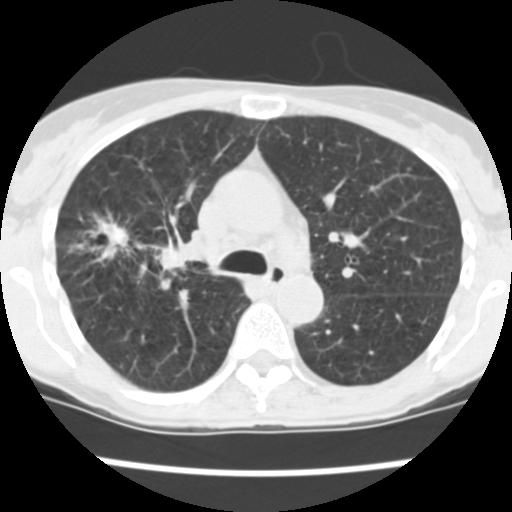
Low-dose screening chest CT, one axial slice; position 163 of 252 along the scan axis; reconstruction kernel STANDARD; 120 kVp; lung window (W 1500 / L -600 HU); 2.5 mm slice thickness; 512 × 512 image matrix, field of view 276 × 276 mm.
Structures marked on this image (manually delineated by an expert):
- lesion 2 (tumor, lower lobe of right lung): box from (x=89, y=218) to (x=203, y=272) px